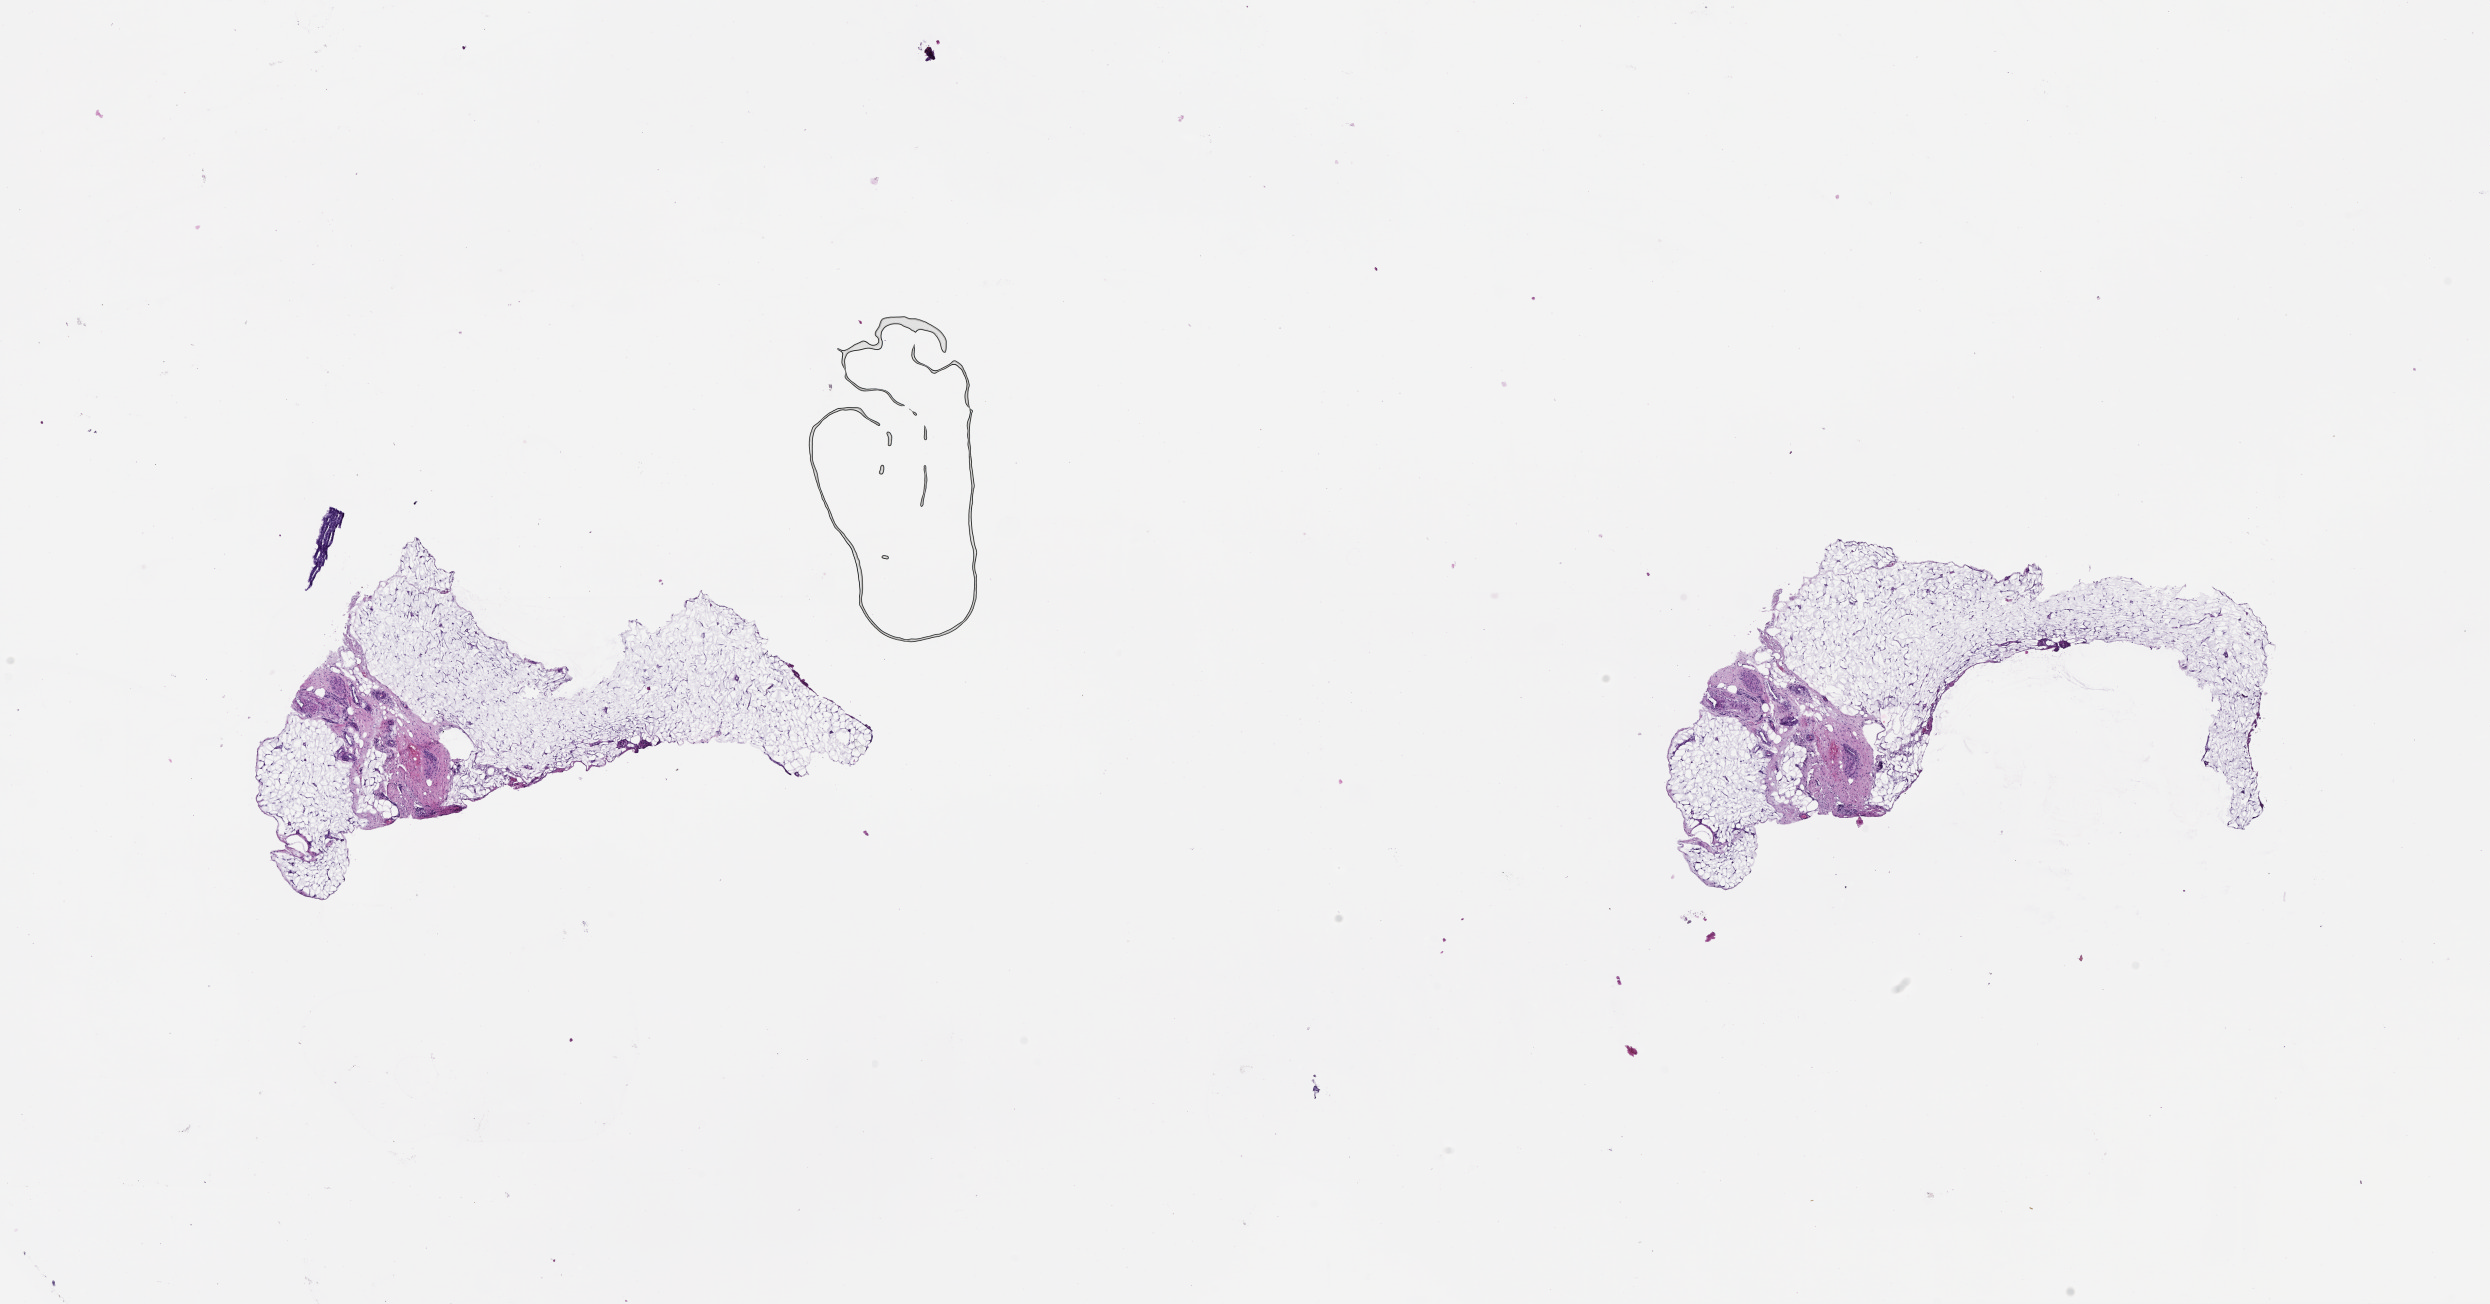
Whole-slide histology image, H&E-stained, a low-resolution overview of the entire scanned area, about 20.0 x 10.5 mm (slide scanned at 20x). 53-year-old male patient.
Patient diagnosis: Malignant melanoma, NOS.